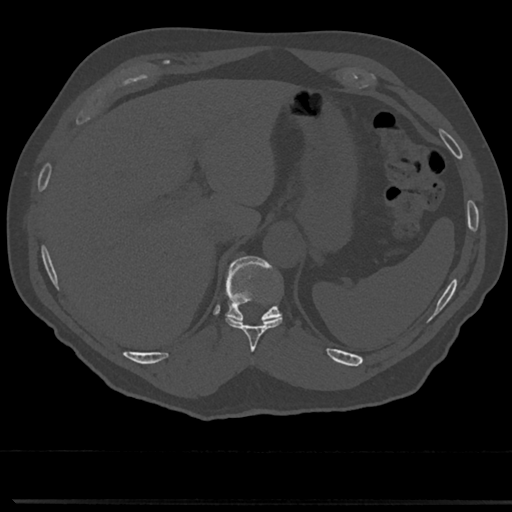
CT including the spine, one axial slice; slice 235 of 817 in the series (ordered by position); reconstruction kernel Br40s/3; 120 kVp; bone window (W 1800 / L 400 HU); 0.5 mm slice thickness; 512 × 512 image matrix. Patient: male, 61 years. From the clinical record (not read from this slice): primary cancer: prostate.
Outlined on this slice (semi-automatically segmented with operator editing):
- T10 vertebra: bounding box [x1, y1, x2, y2] px = [225, 281, 283, 350]
- T11 vertebra: [227, 258, 282, 322]